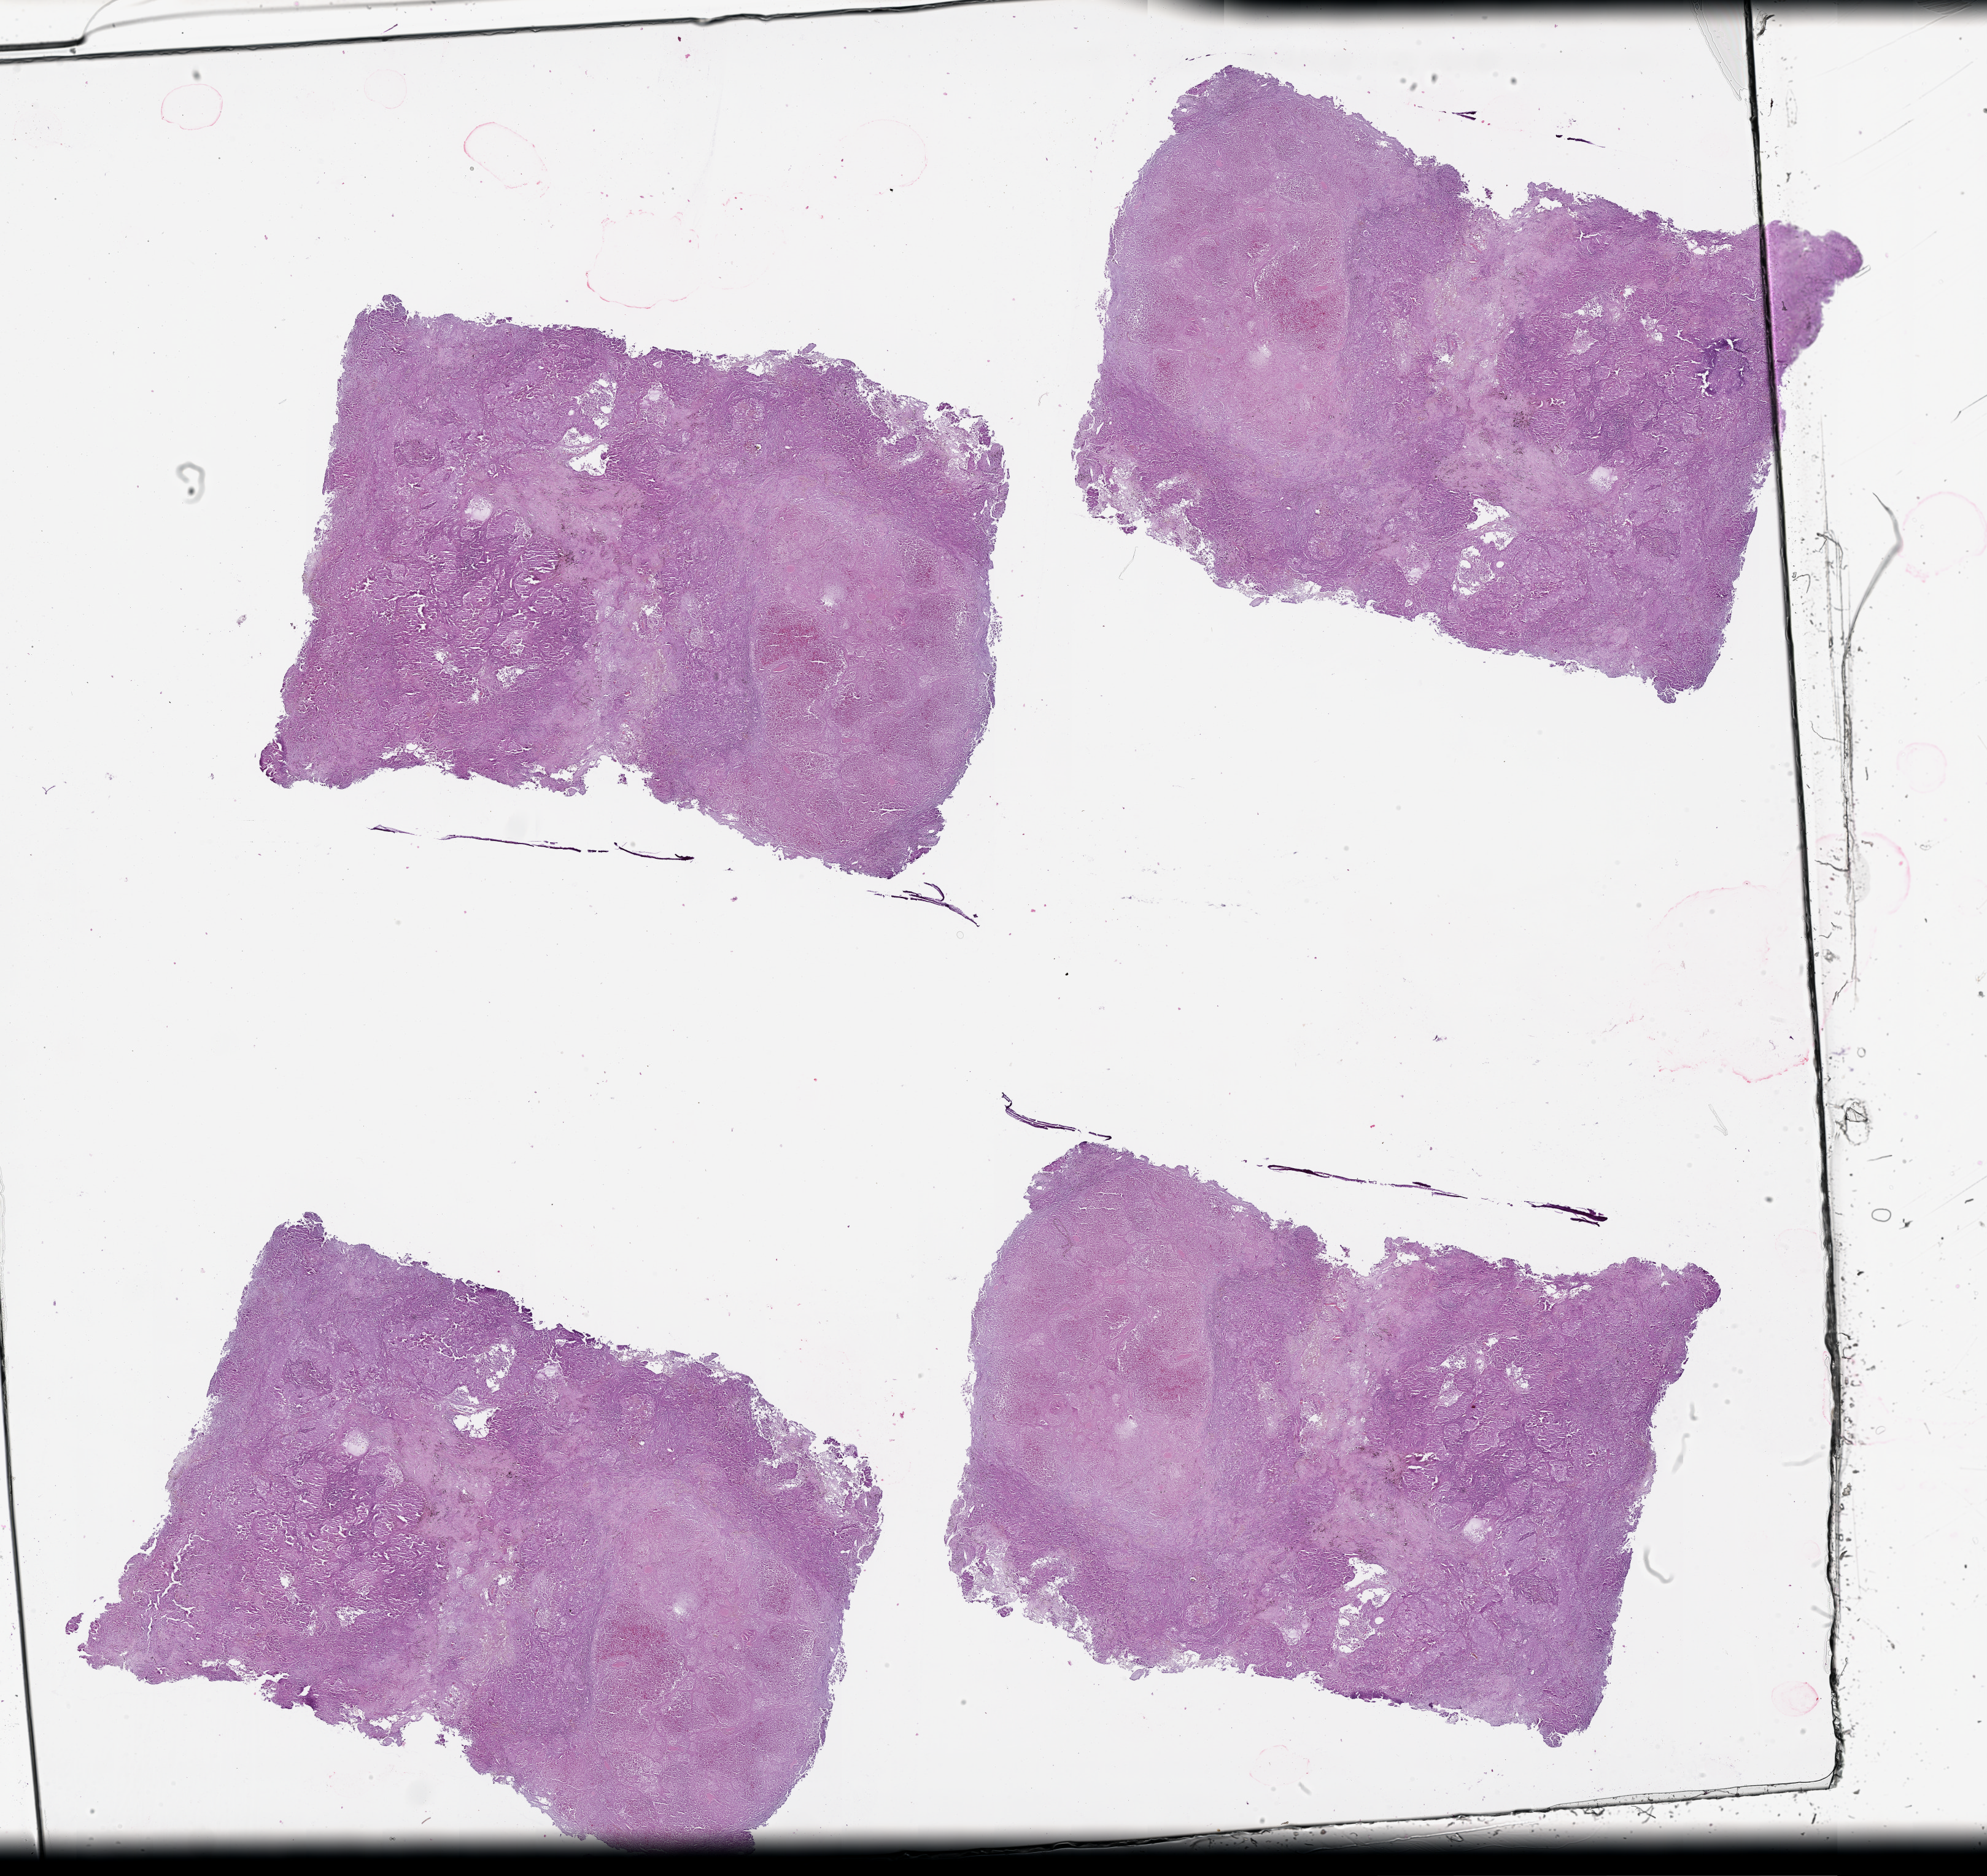
Digitized H&E tissue section (whole slide) — a low-resolution overview of the entire scanned area, about 26.1 x 24.6 mm (acquisition: 20x scan); tumour tissue sample, lung. 61-year-old male patient.
* patient diagnosis (cohort enrolment): squamous cell carcinoma (lung)